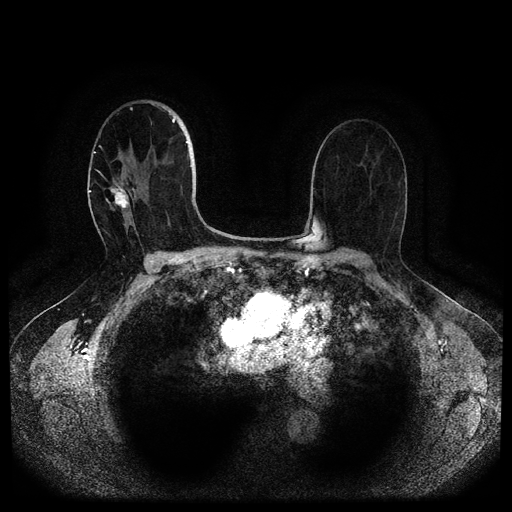
Breast MRI (dynamic contrast-enhanced, multi-phase), one axial slice. Position 63 of 116 along the scan axis. Dynamic contrast-enhanced series, time point 2 of 5 at this slice position (early post-contrast). 1.5 T. TE 2.6 ms, TR 5.3 ms. 2 mm slice thickness. 512 × 512 image matrix, field of view 350 × 350 mm. Patient: female, 82 years.
Structures marked on this image (semi-automatically segmented with operator editing):
- breast lesion (labelled 'tumour' in the annotation; benign lesions carry a separate 'benign' label): bounding box (x1, y1, x2, y2) in pixels: (110, 184, 130, 212)